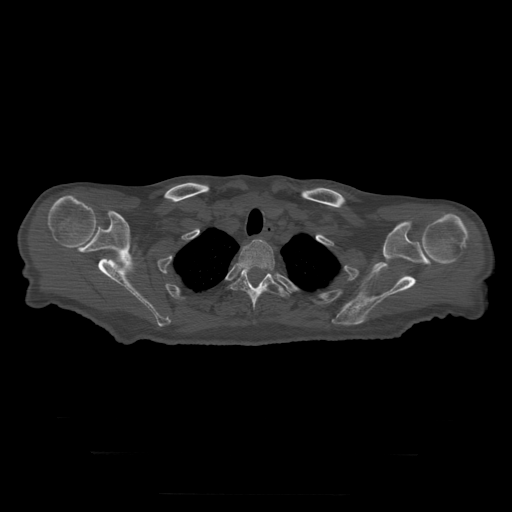
CT including the spine, one axial slice; slice 264 of 397 in the series (ordered by position); reconstruction kernel STANDARD; 120 kVp; bone window (W 1800 / L 400 HU); 512 × 512 image matrix, field of view 510 × 510 mm. Patient age 73 years. Case-level facts recorded for this patient, not image findings: primary cancer: prostate.
Outlined on this slice (semi-automatic segmentation, software-assisted and operator-edited):
- T2 vertebra: box from (x=239, y=239) to (x=275, y=270) px
- T3 vertebra: (x=231, y=268)–(x=289, y=311)